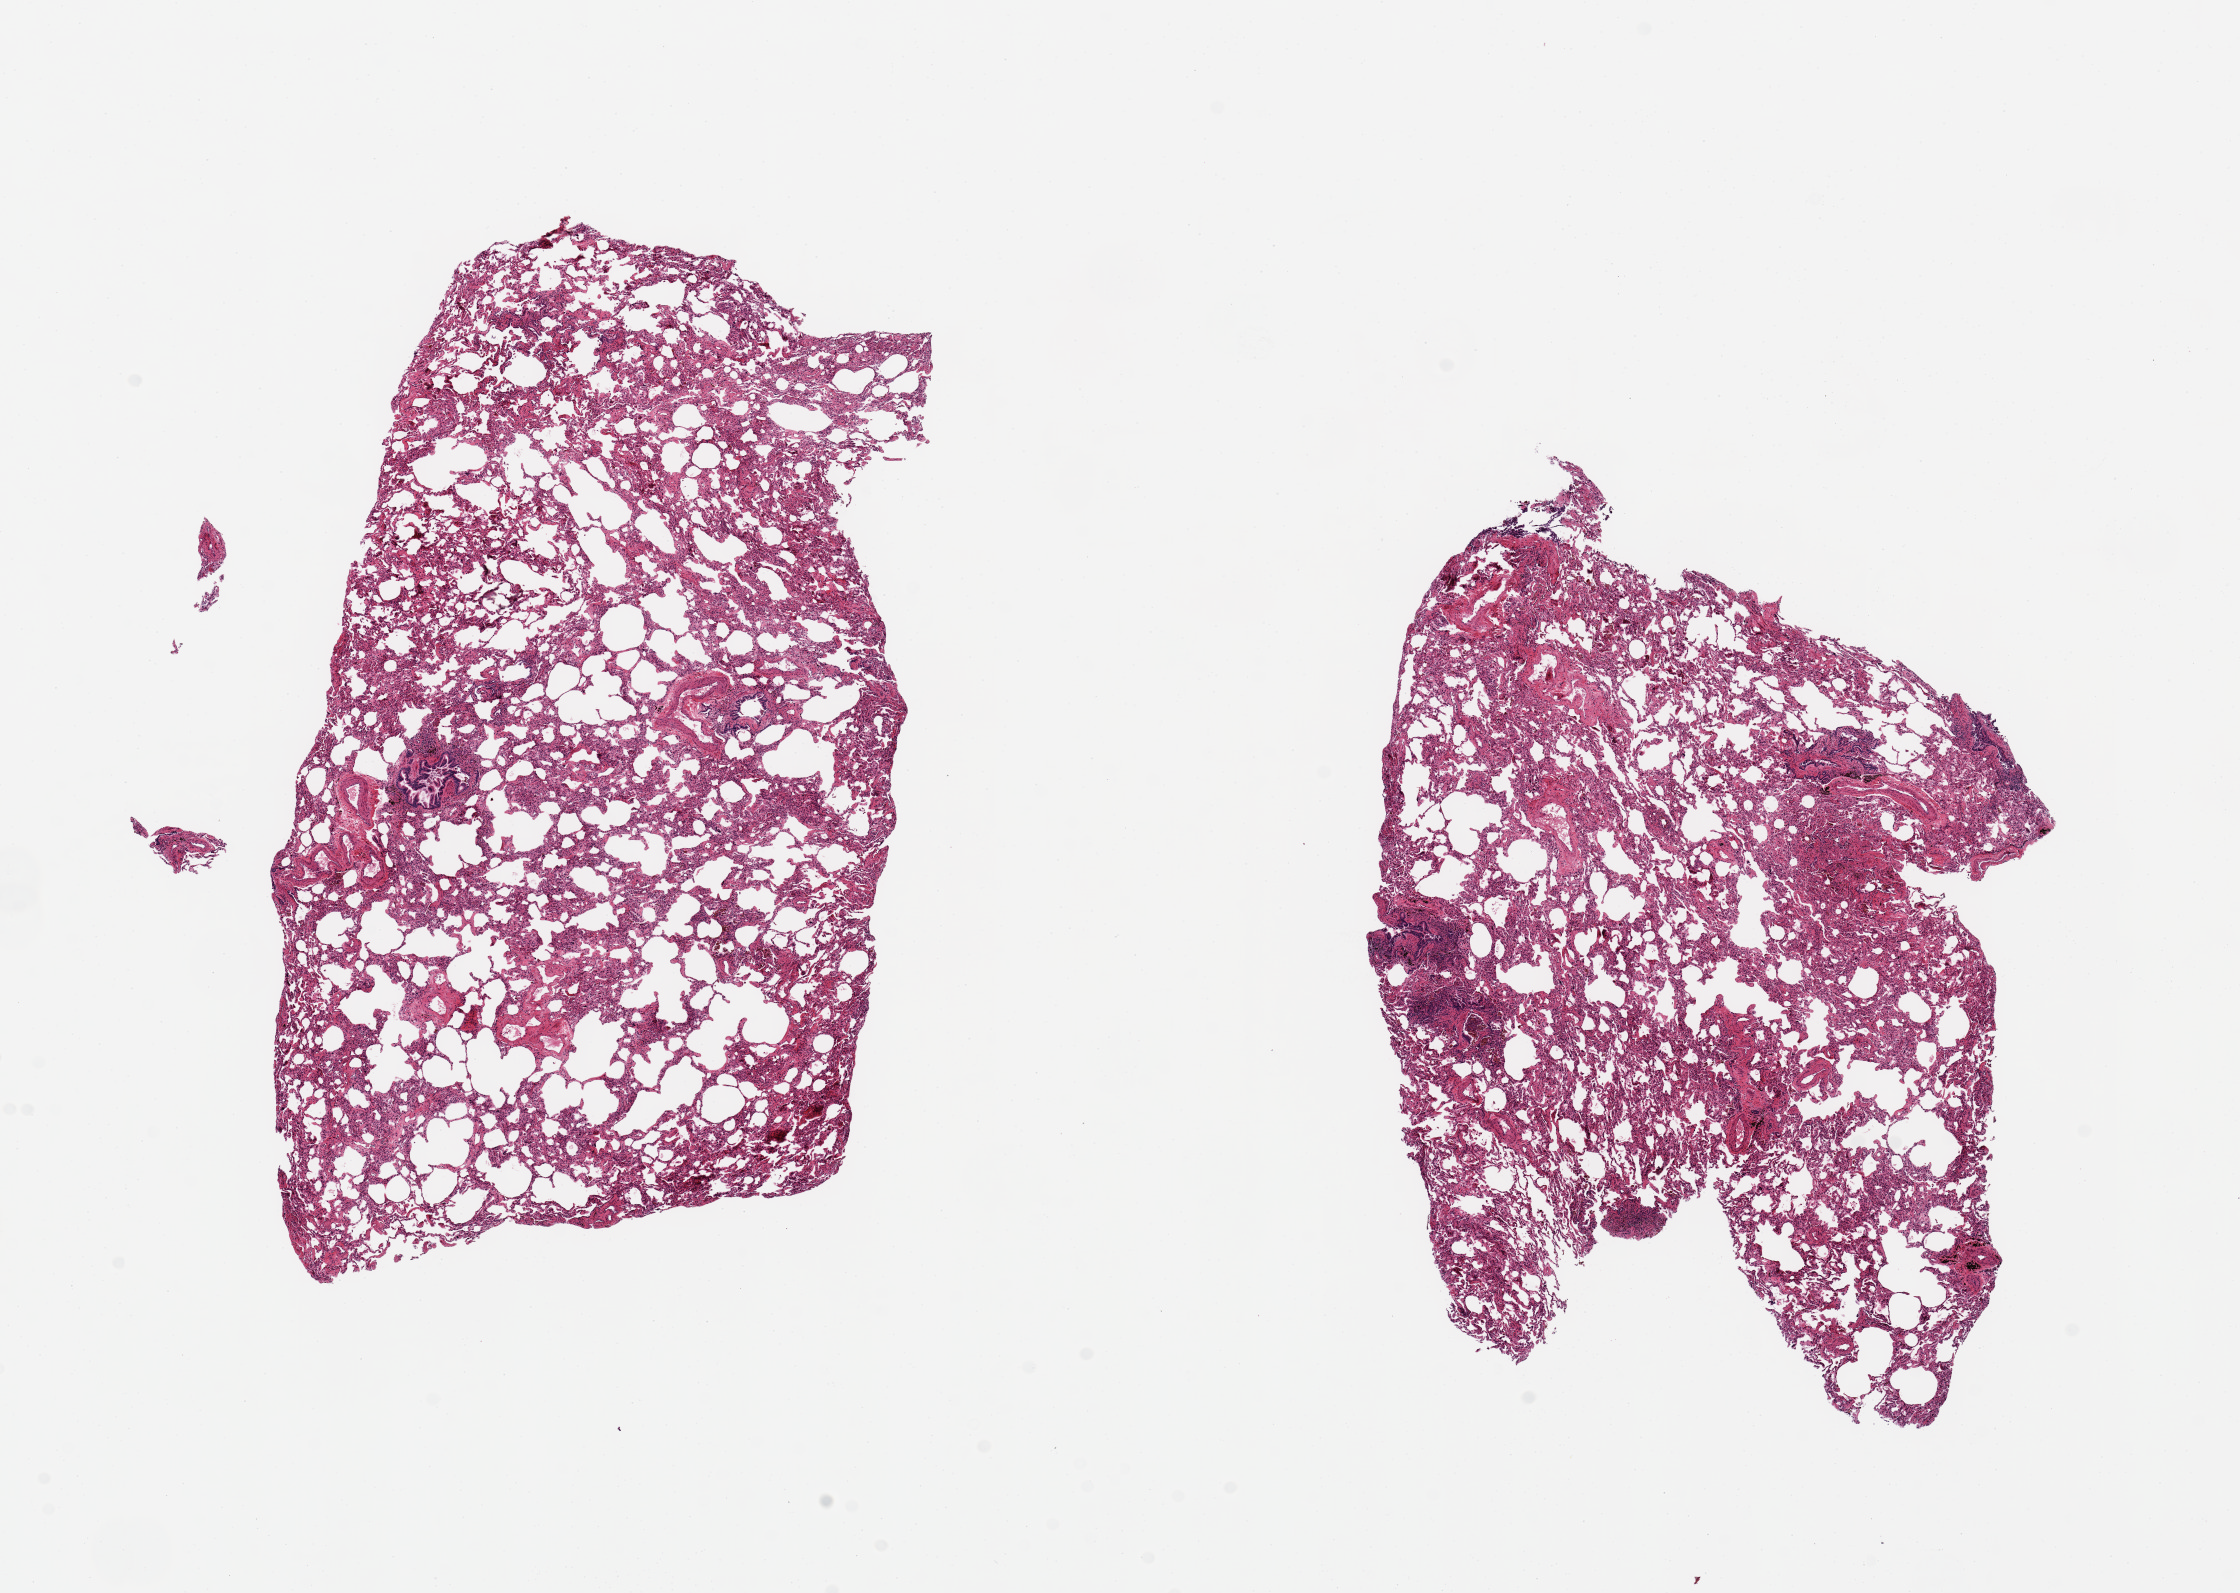
Hematoxylin and eosin (H&E) whole-slide image, whole scanned area (about 17.7 x 12.6 mm, acquisition: 20x scan) shown as a low-resolution overview. PAXgene-fixed paraffin-embedded (PFPE) section. Sampled site (target tissue): lung. Tissue donor sample. Female donor.
Reviewer comment on this tissue sample: 2 ~7x5mm pieces. Chronic congestion, ? diffuse alveolar damage sequence.